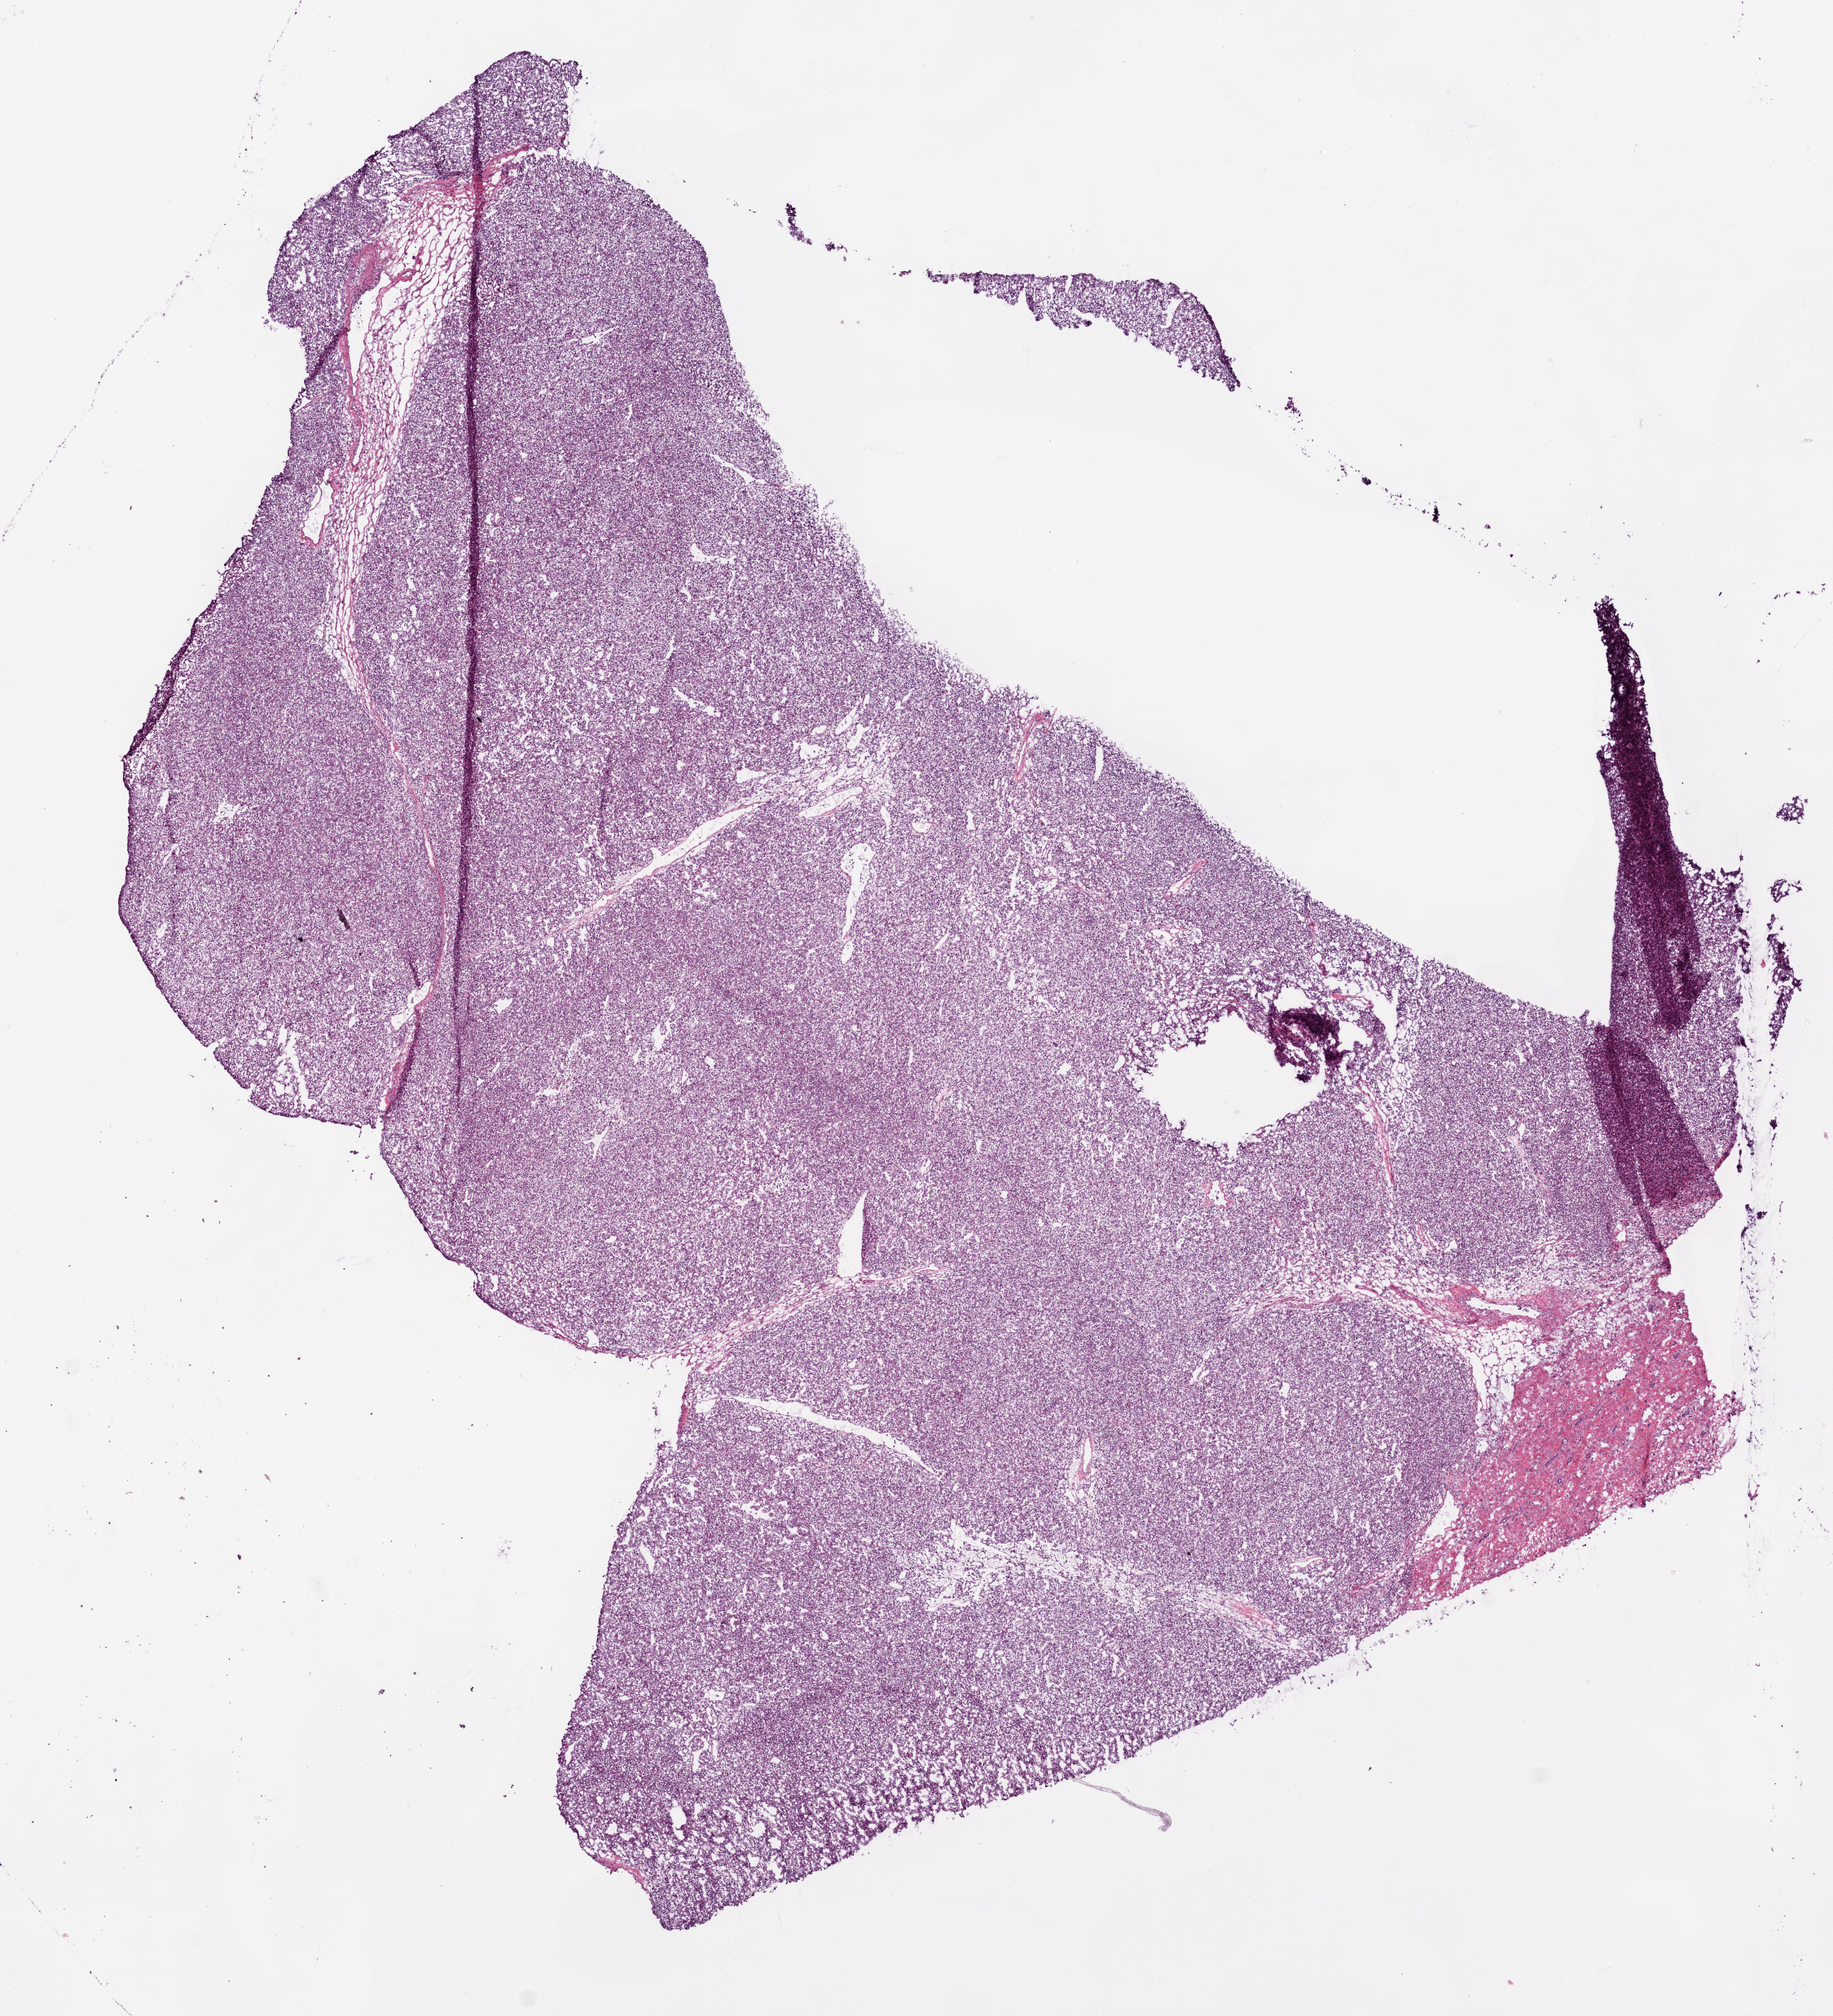
Hematoxylin and eosin (H&E) stained whole-slide image — whole scanned area (about 9.0 x 9.9 mm, slide scanned at 20x) shown as a low-resolution overview, frozen section from the bottom of the tissue portion, kidney, primary tumour sample. Female patient; age at initial diagnosis 63 years. Slide review estimates, as recorded: tumour cells 90%, tumour nuclei 90%.
Histologic diagnosis: Clear cell adenocarcinoma, NOS.